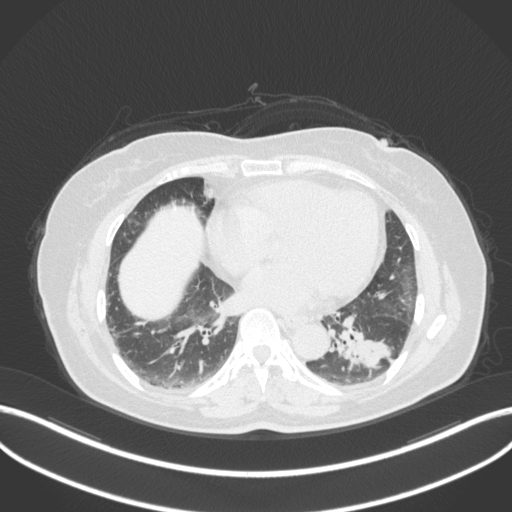
Chest CT, one axial slice. Position 147 of 307 along the scan axis. Reconstruction kernel B31f. Lung window (W 1500 / L -600 HU). 512 × 512 image matrix, field of view 400 × 400 mm. Patient: female, 59 years. Case-level facts recorded for this patient, not image findings: clinical TNM (as recorded): T2a N0 M0; histopathological grade: G2-3.
Structures marked on this image (bounding box drawn by a radiologist):
- lung tumour (recorded histology: adenocarcinoma): bounding box (x1, y1, x2, y2) in pixels: (330, 314, 396, 373)